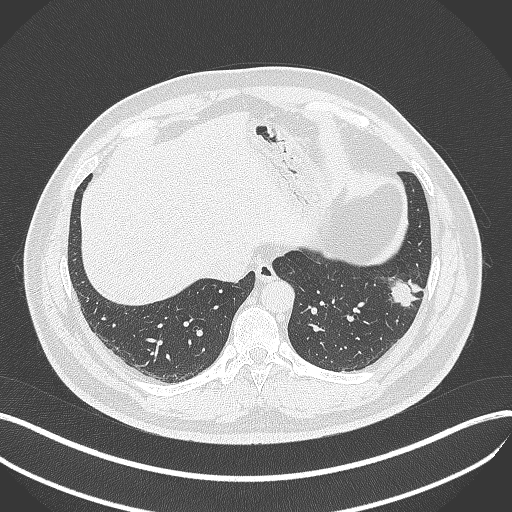
Chest CT, one axial slice; position 114 of 429 along the scan axis; reconstruction kernel B70f; lung window (W 1500 / L -600 HU); 512 × 512 image matrix, field of view 400 × 400 mm. Male patient, age 39 years. From the clinical record (not read from this slice): clinical TNM (as recorded): T2a N0 M0; histopathological grade: G2-3.
Outlined on this slice (rectangle marked by the reading radiologist):
- lung tumour (recorded histology: adenocarcinoma): bounding box (x1, y1, x2, y2) in pixels: (382, 271, 427, 315)